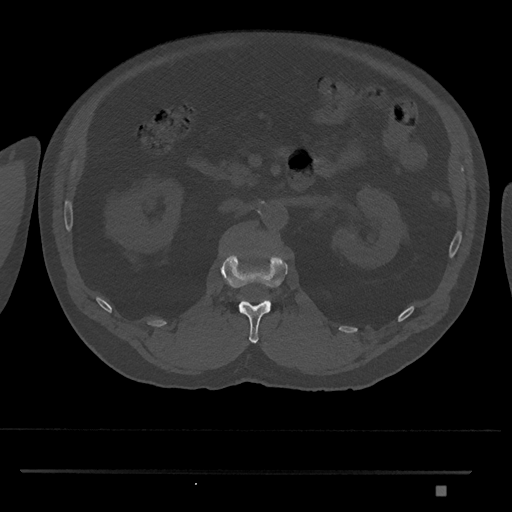
CT including the spine, one axial slice; position 803 of 1134 along the scan axis; reconstruction kernel Br40s/3; 120 kVp; bone window (W 1800 / L 400 HU); 0.5 mm slice thickness; 512 × 512 image matrix, field of view 429 × 429 mm. Male patient, age 65 years. From the clinical record (not read from this slice): primary cancer: prostate.
Annotated regions visible in this slice (semi-automatic segmentation, software-assisted and operator-edited):
- L1 vertebra: box from (x=220, y=252) to (x=288, y=343) px